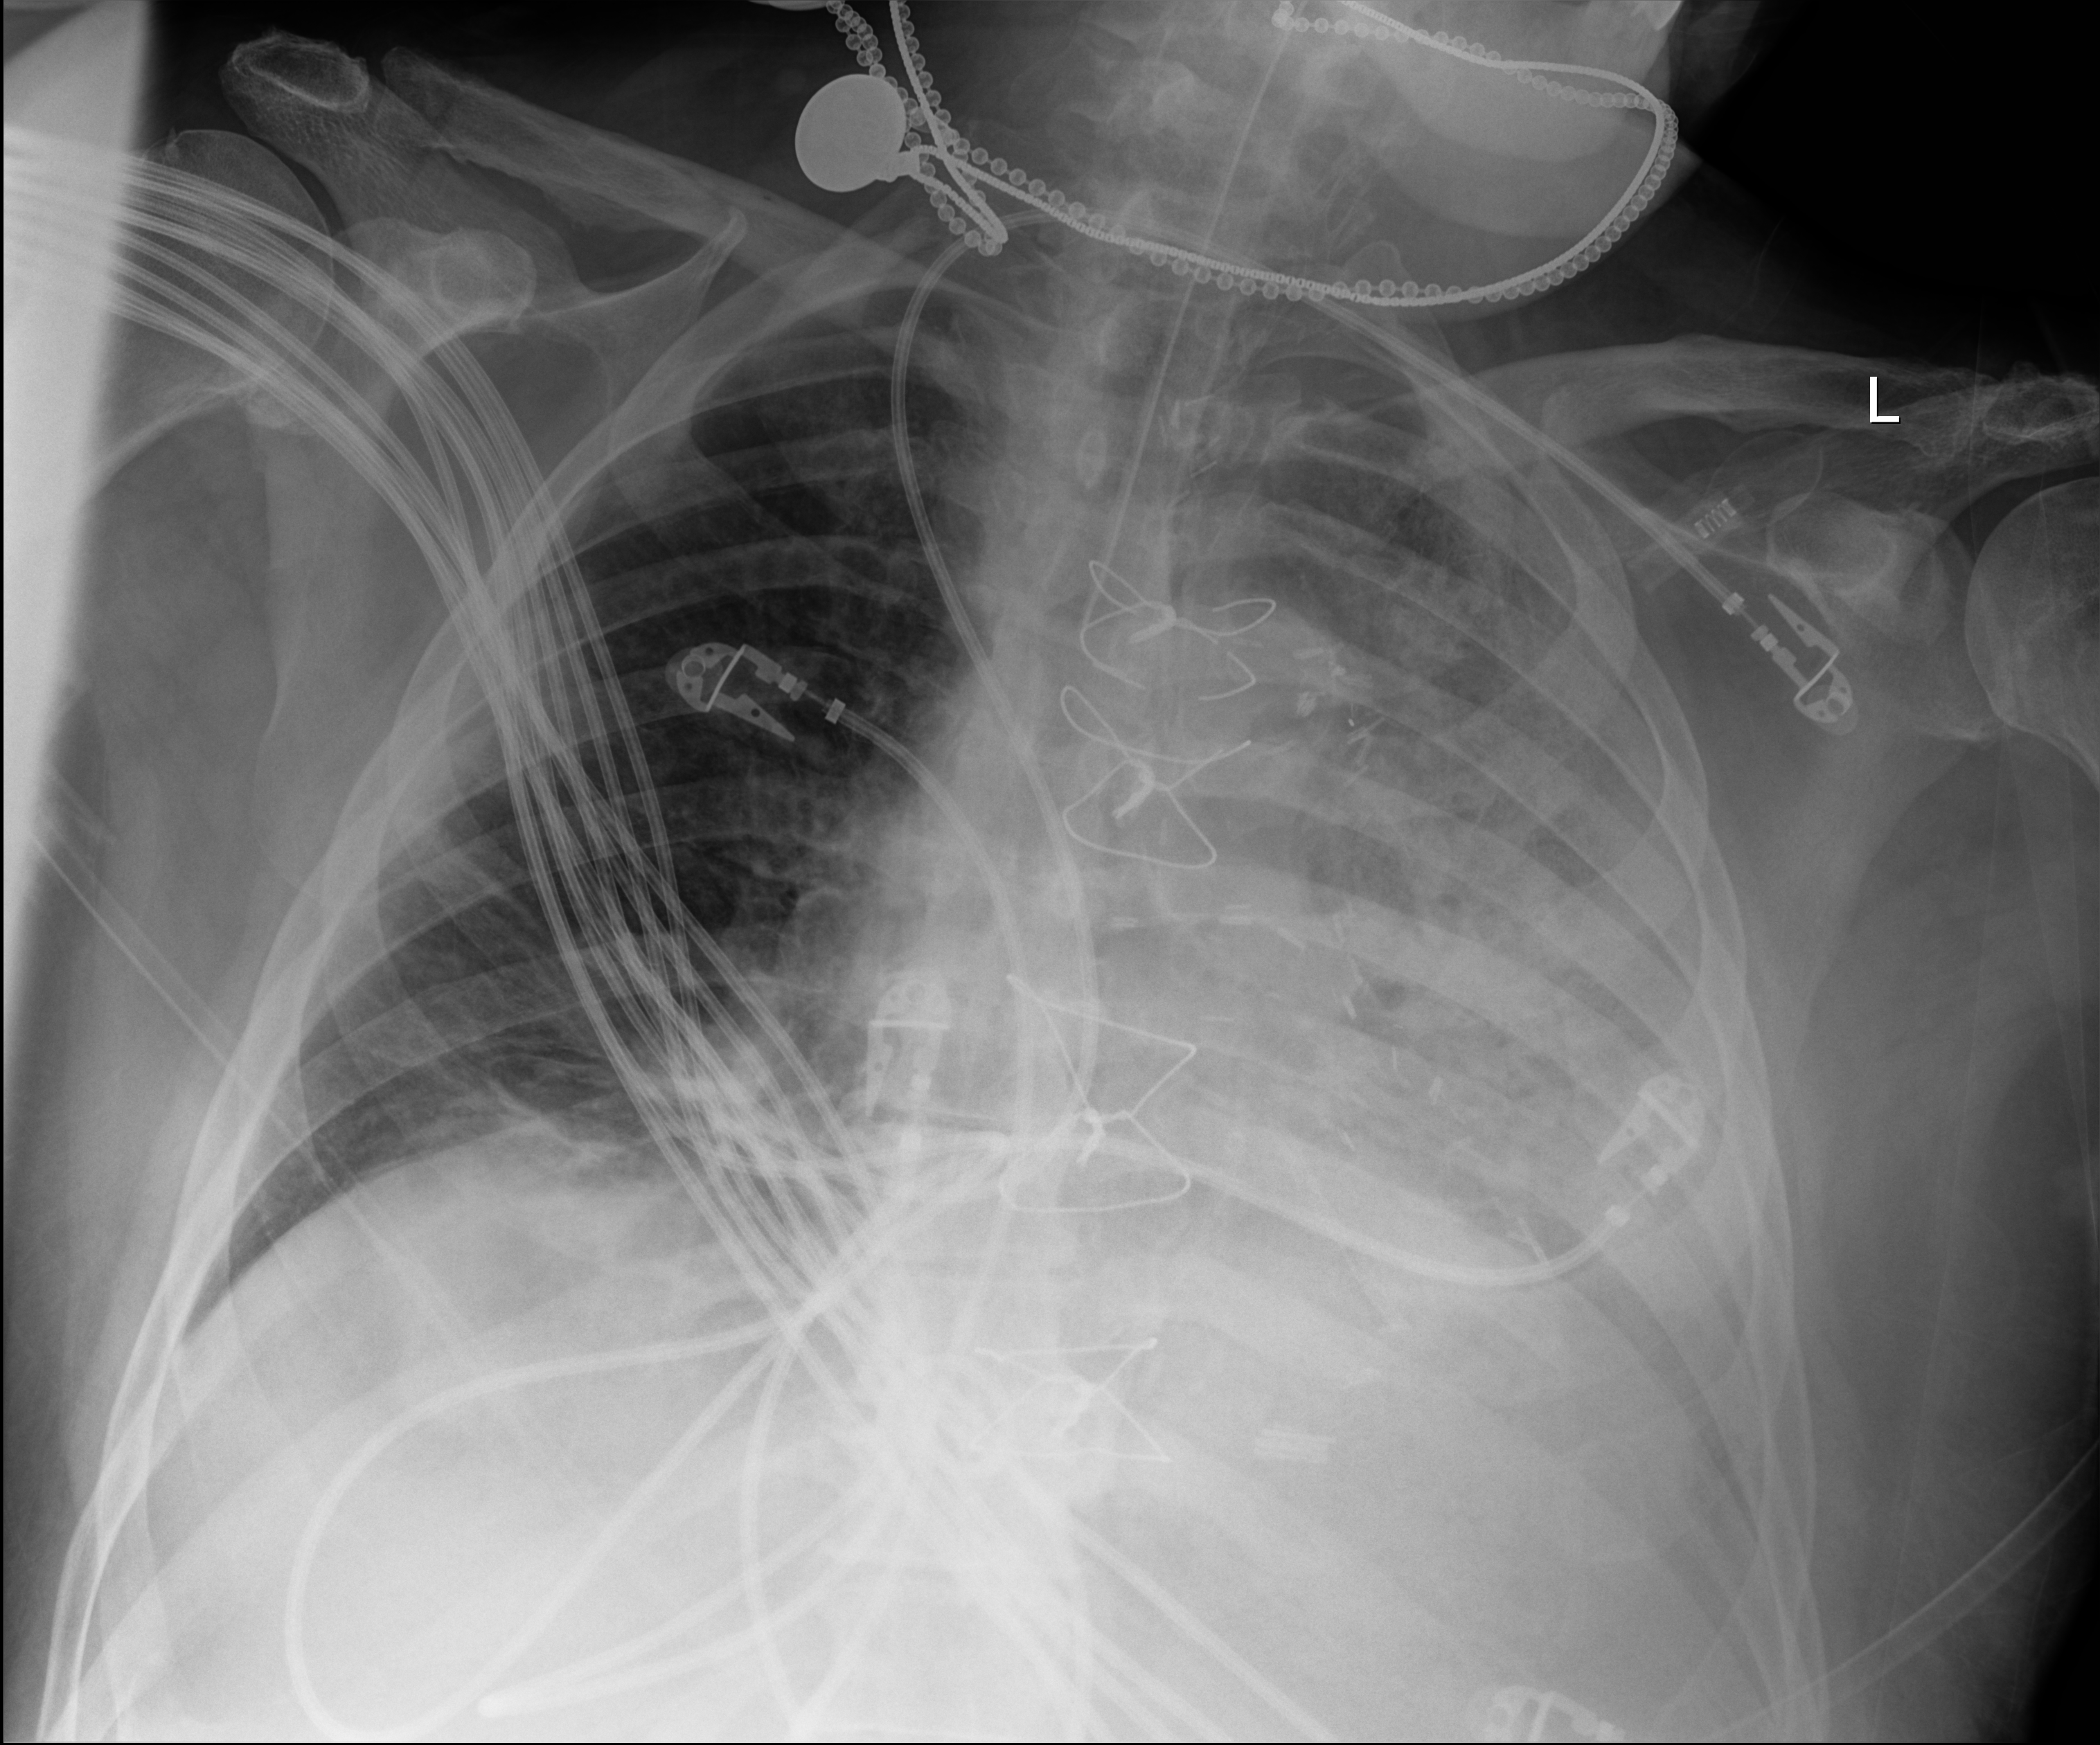
Chest X-ray (portable); anteroposterior (AP) projection. Patient hospitalised with COVID-19; male, aged 60–74 years.
Hospital-stay facts (about this admission, not read from this image; timing relative to this image not recorded): mechanically ventilated during this hospital stay: yes.